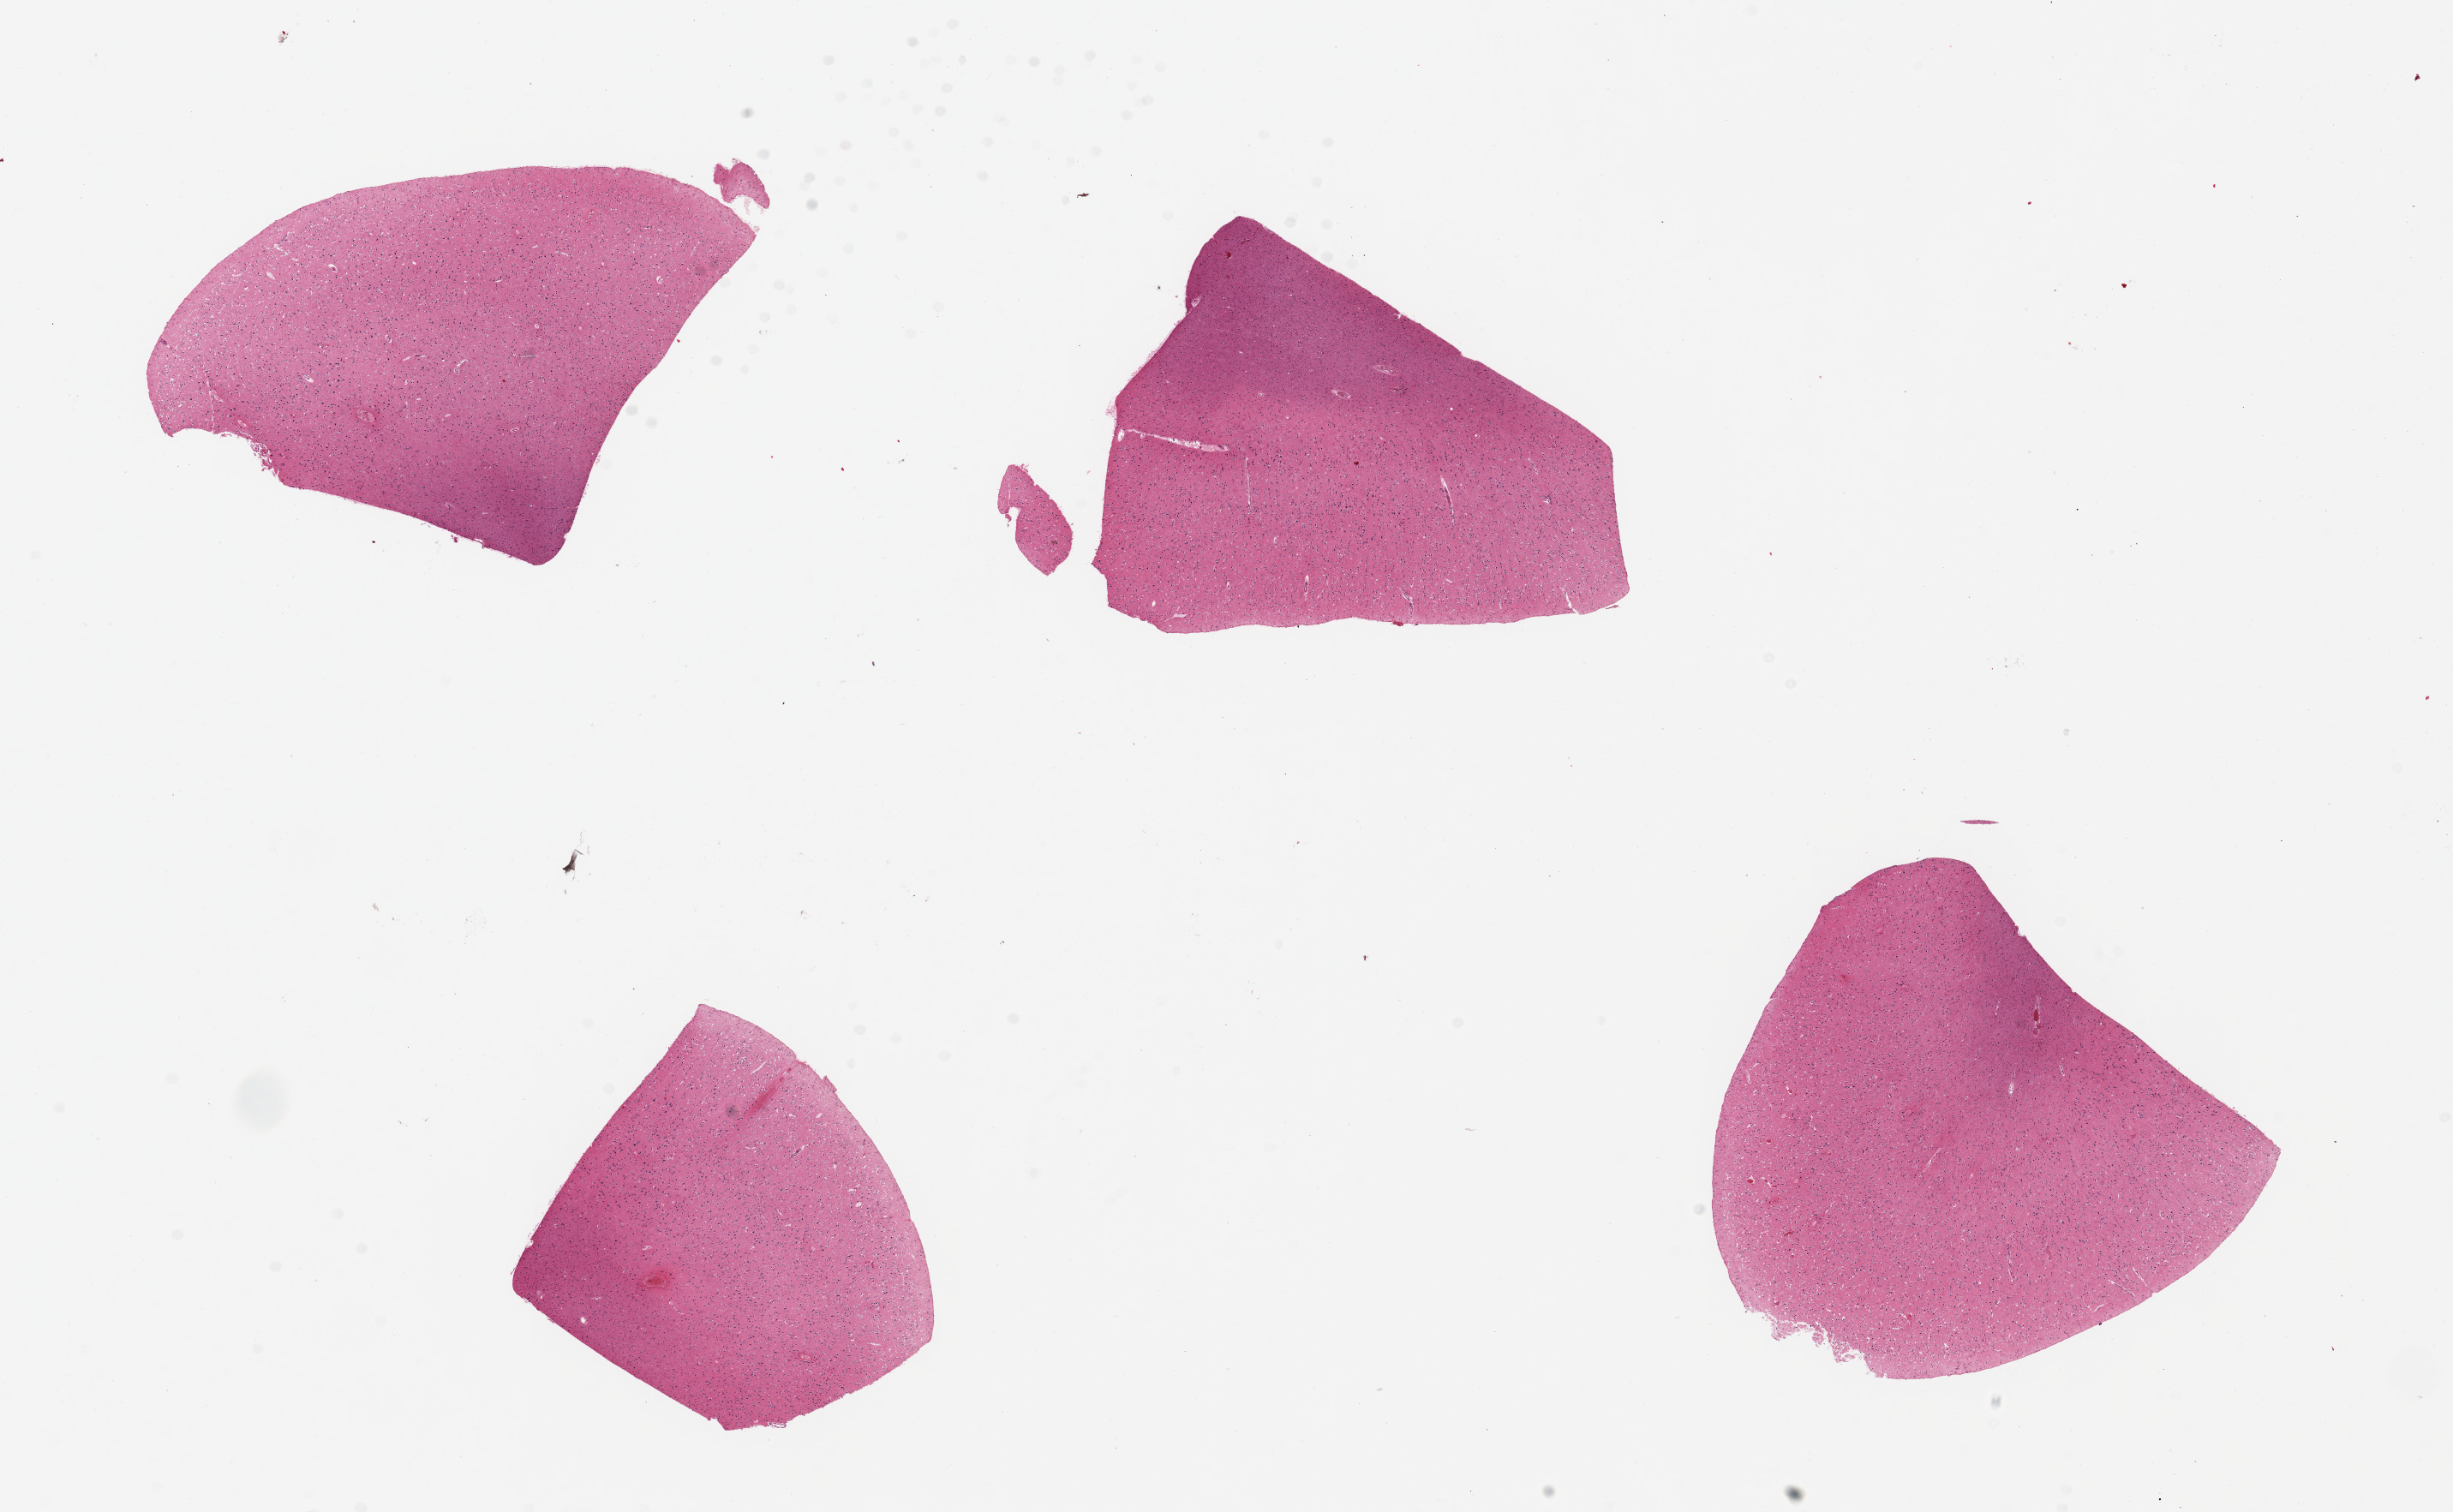
Whole-slide image, haematoxylin and eosin stain, brightfield — whole scanned area (about 22.6 x 14.0 mm) shown as a low-resolution overview; PAXgene-fixed paraffin-embedded (PFPE) section; sampled site (target tissue): cerebral cortex; donor tissue sample. Female donor.
Pathologist's review note for this sample: 4 pieces ~4x4mm.